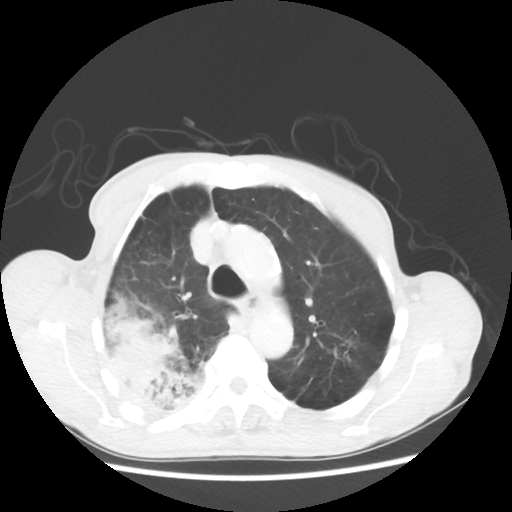
Chest CT, one axial slice; slice 40 of 58 in the series (ordered by position); 100 kVp; lung window (W 1500 / L -600 HU); 512 × 512 image matrix. Patient: male, 75 years. From the clinical record (not read from this slice): clinical TNM (as recorded): T4 N1 M1.
Annotated regions visible in this slice (bounding box drawn by a radiologist):
- lung tumour (recorded histology: adenocarcinoma): box from (x=92, y=290) to (x=208, y=411) px